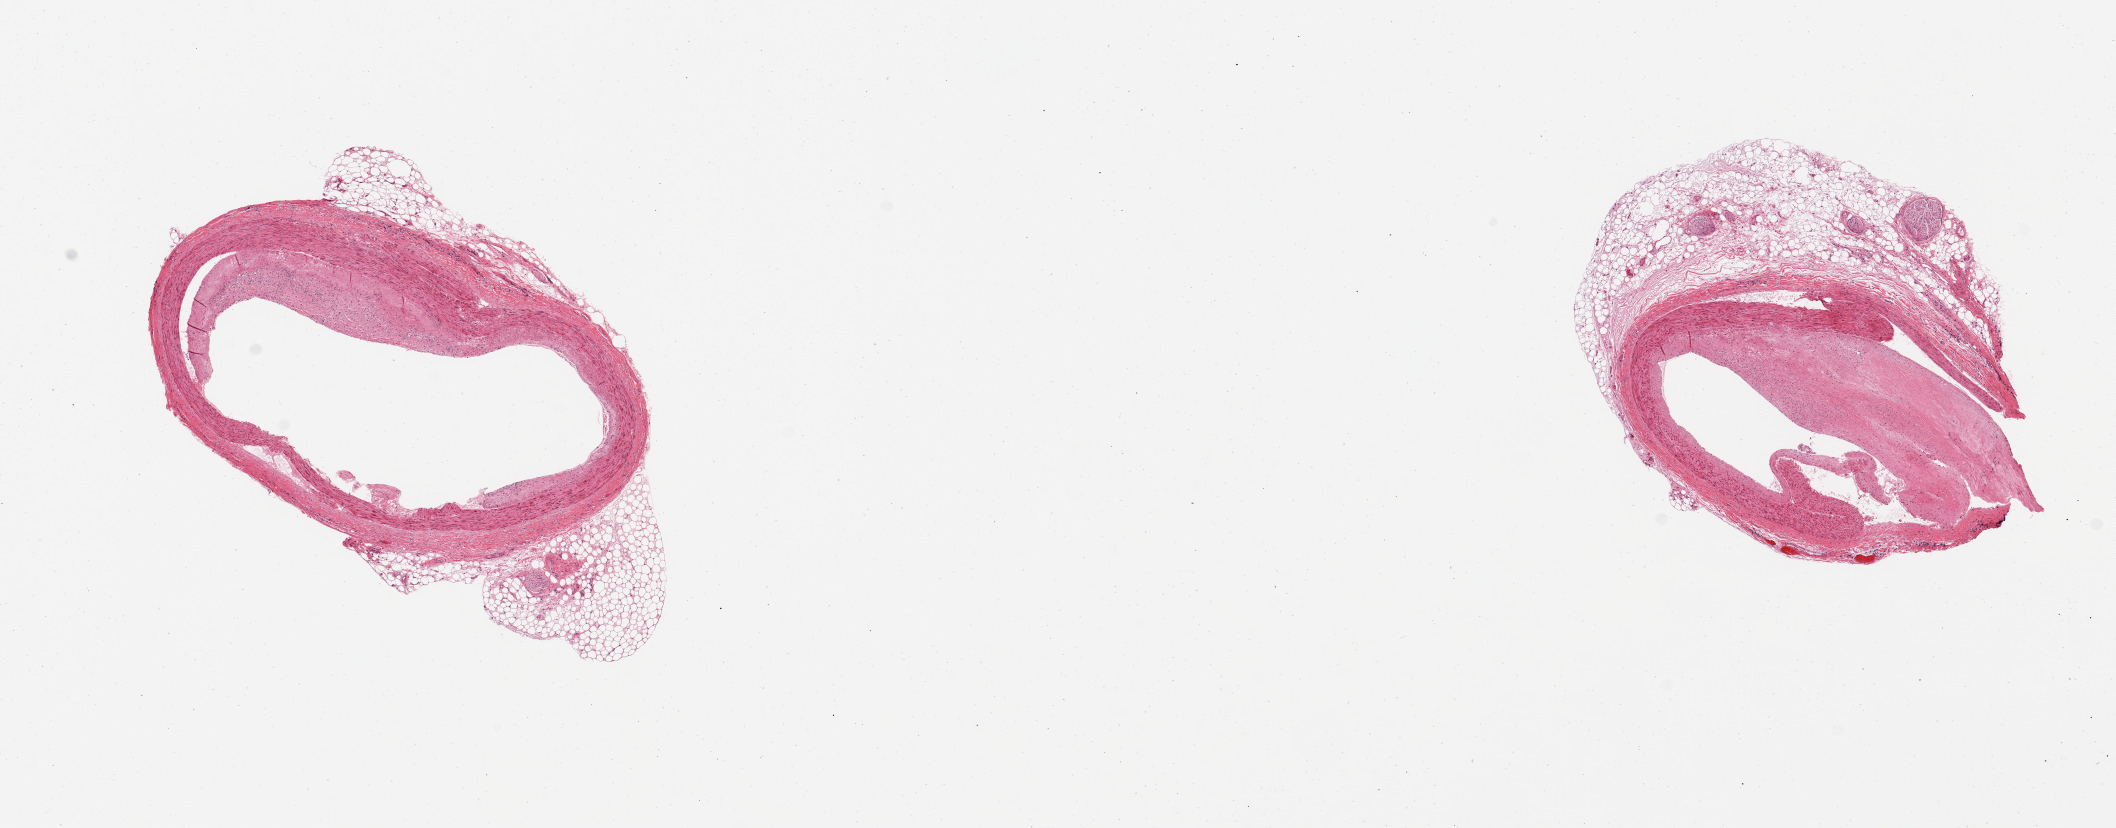
Whole-slide image, hematoxylin and eosin (H&E) stain — whole scanned area (about 16.7 x 6.5 mm, slide scanned at 20x) shown as a low-resolution overview; PAXgene-fixed, paraffin-embedded tissue; target tissue: coronary artery; donor tissue sample. Donor: male.
Review note (as recorded): 2 pieces; eccentric atheromatous plaques; 50% external untrimmed fat.